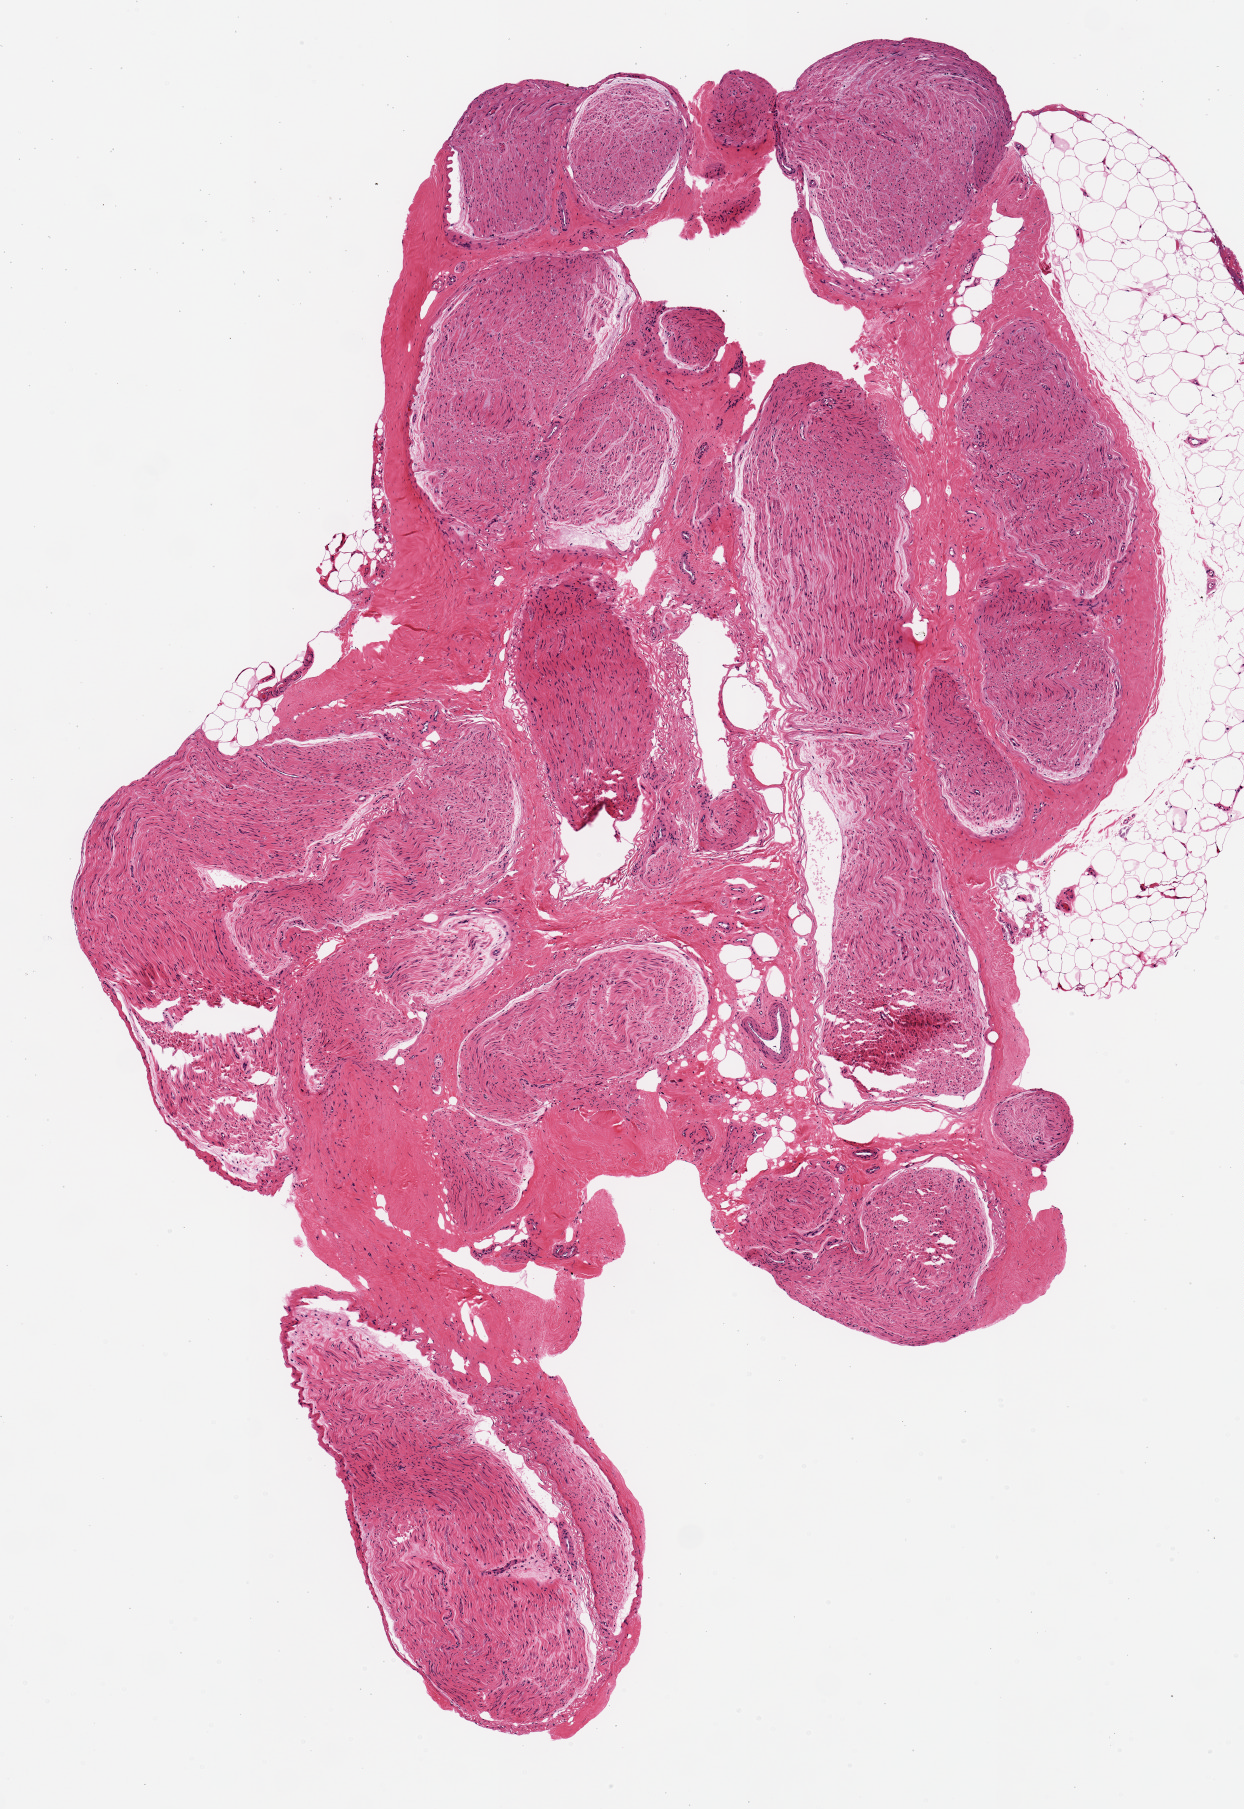
Whole-slide image, H&E stain, whole scanned area (about 4.9 x 7.2 mm, from a 20x scan) shown as a low-resolution overview, PAXgene-fixed, paraffin-embedded tissue, section of tibial nerve (target tissue), donor tissue sample.
Review note (as recorded): 1 piece 6x4 mm.